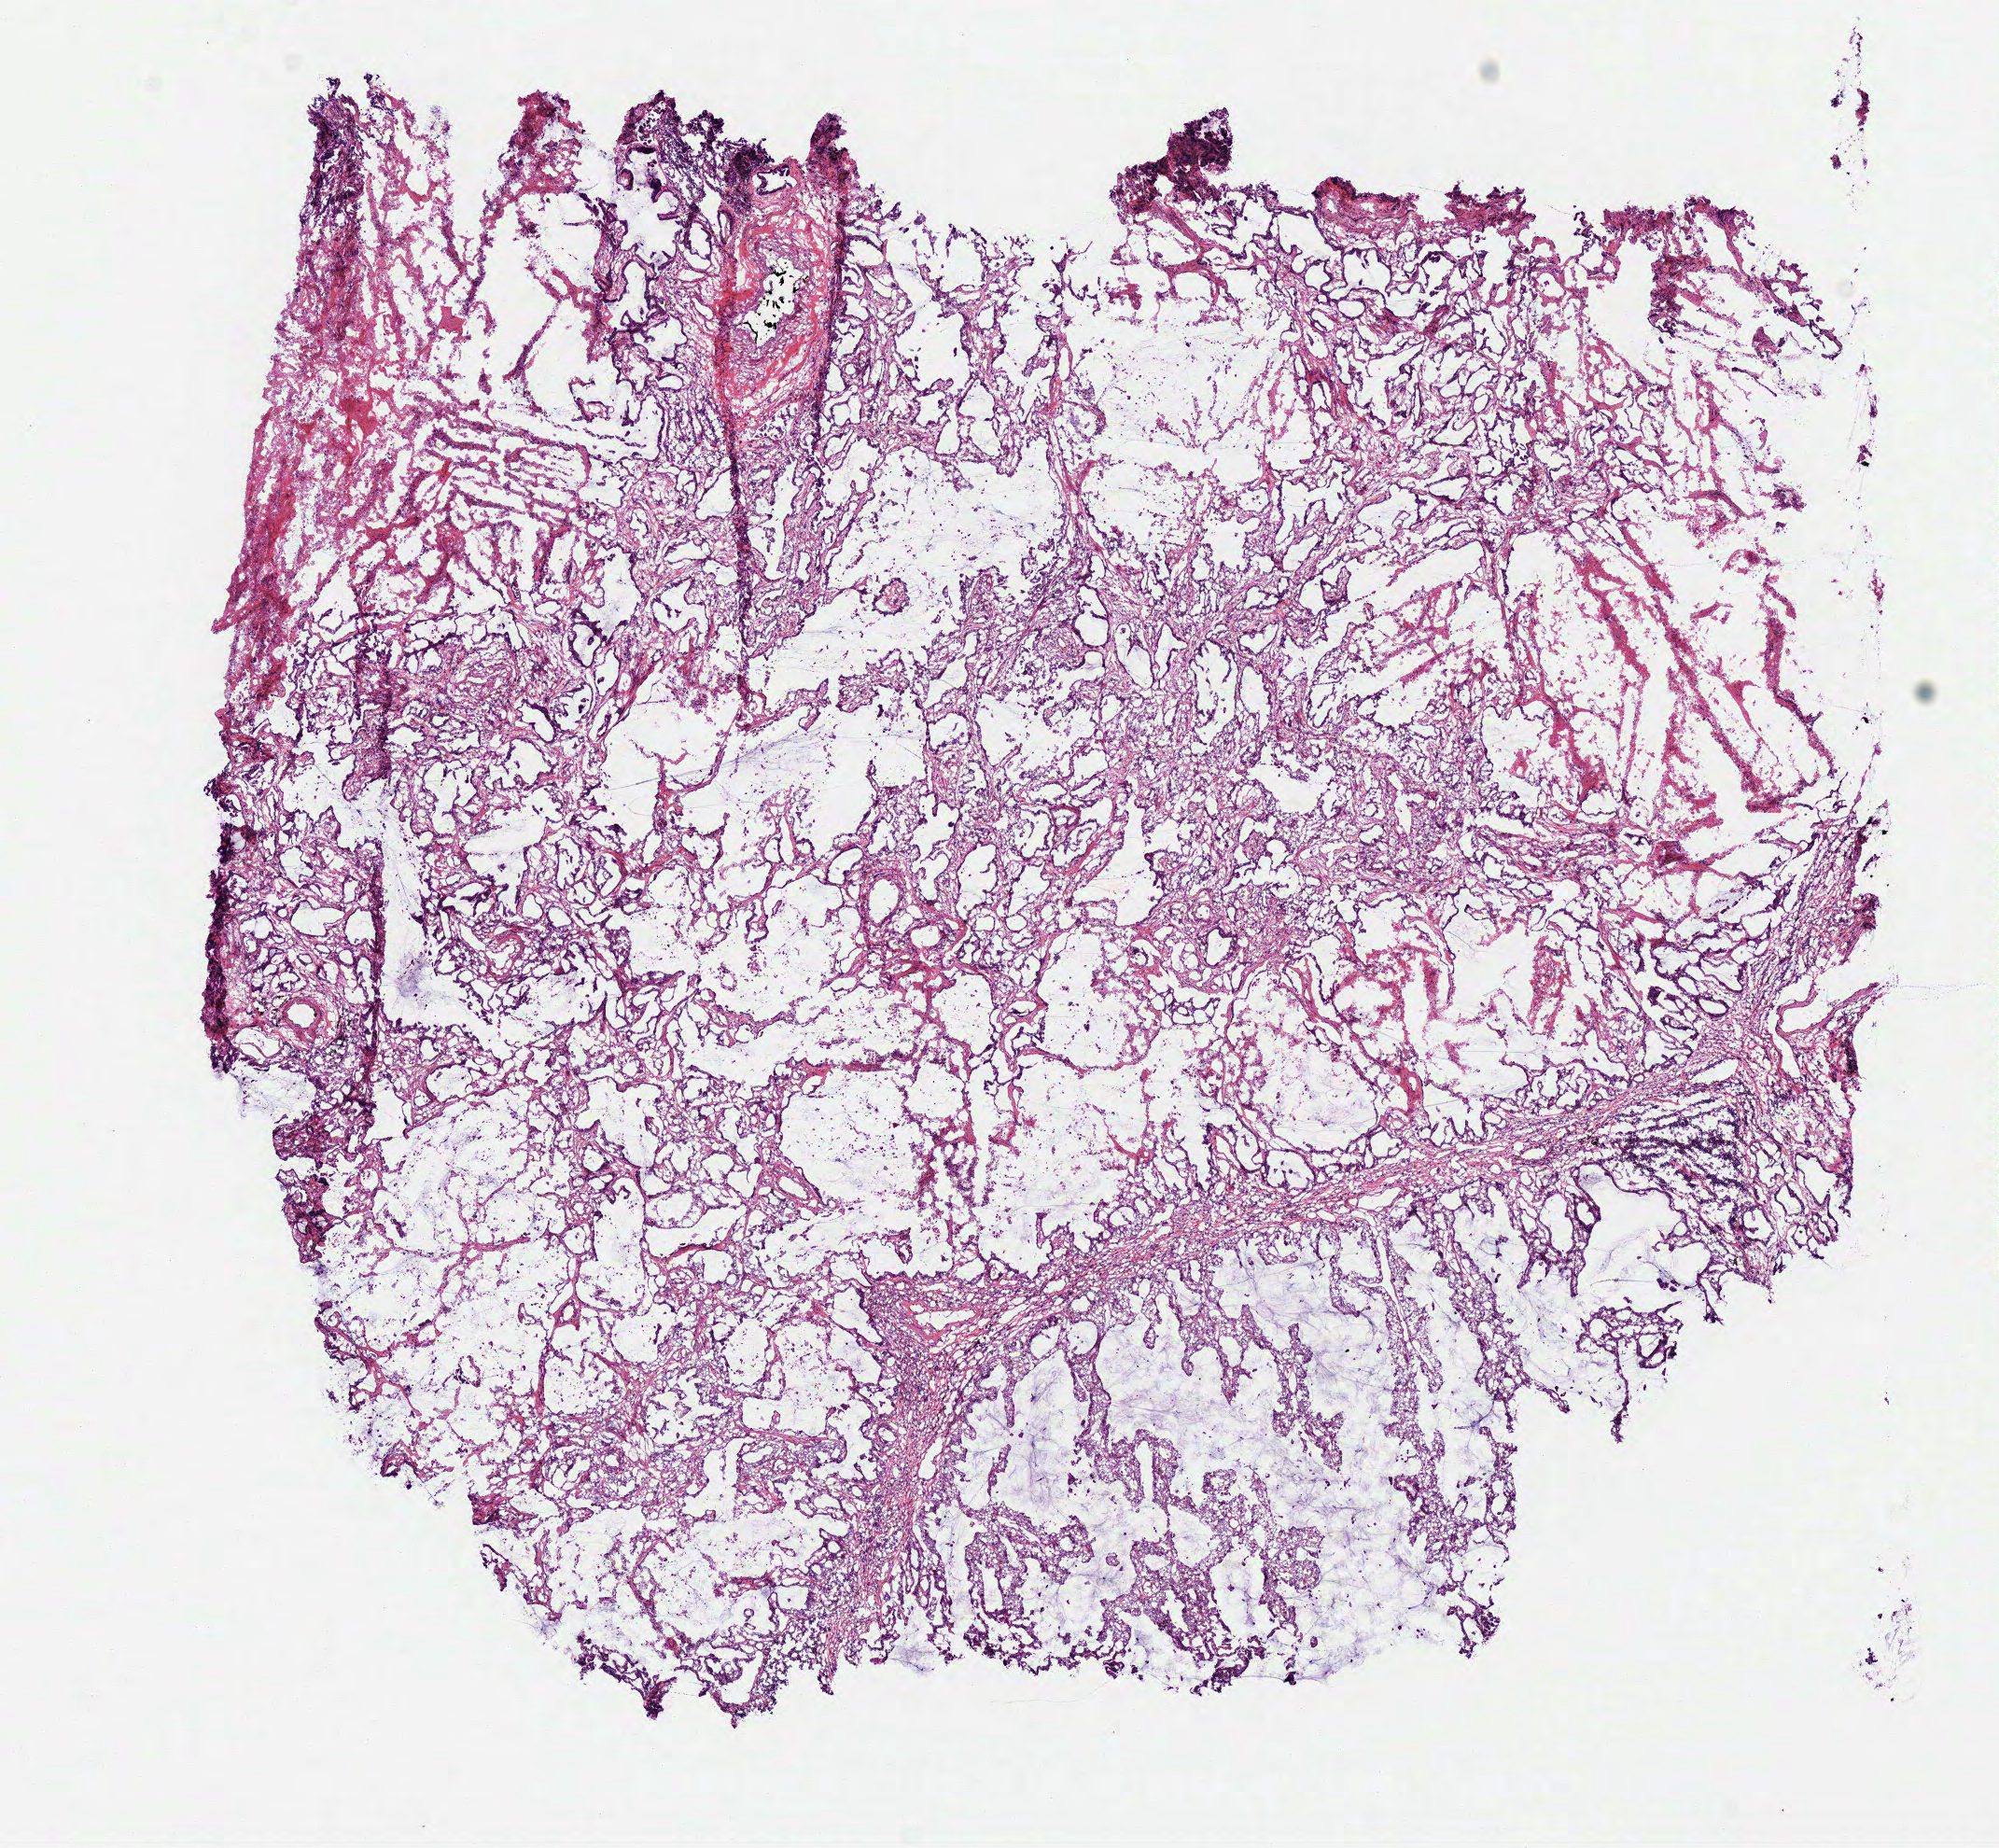
Whole-slide histology image, H&E-stained, a low-resolution overview of the entire scanned area, about 8.4 x 7.8 mm, frozen section, lung, primary tumour sample. Male, age 84 years at initial diagnosis. Pathologist review of this section (percent, as recorded): tumour cells 67%, tumour nuclei 70%, normal cells 0%, stromal cells 15%, necrosis 18%.
AJCC pathologic stage: IIB (6th edition). Diagnosis: Adenocarcinoma, NOS (lower lobe, lung). Laterality: left.